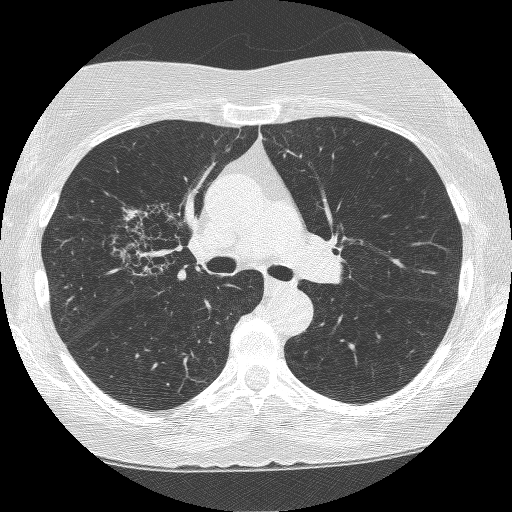
Low-dose screening chest CT, axial slice; second annual screen; lung window (W 1500 / L -600 HU); 1.25 mm slice thickness; lung (sharp) reconstruction kernel (BONE); slice 152 of 249 in the series; 512 × 512 image matrix. Female, age 64 years at enrolment. Former smoker at enrolment.
Expert-annotated lung lesion, box from (x=115, y=205) to (x=205, y=290) px. The screening reader recorded 4 non-calcified nodules or masses ≥4 mm on this exam (right upper lobe, right upper lobe, right upper lobe, left upper lobe); which of them this box marks is not recorded. Participant outcome: lung cancer diagnosed 381 days after this screen — adenocarcinoma, NOS, right upper lobe, right middle lobe, right hilum, stage IV (AJCC 6th edition), 85 mm at pathology.